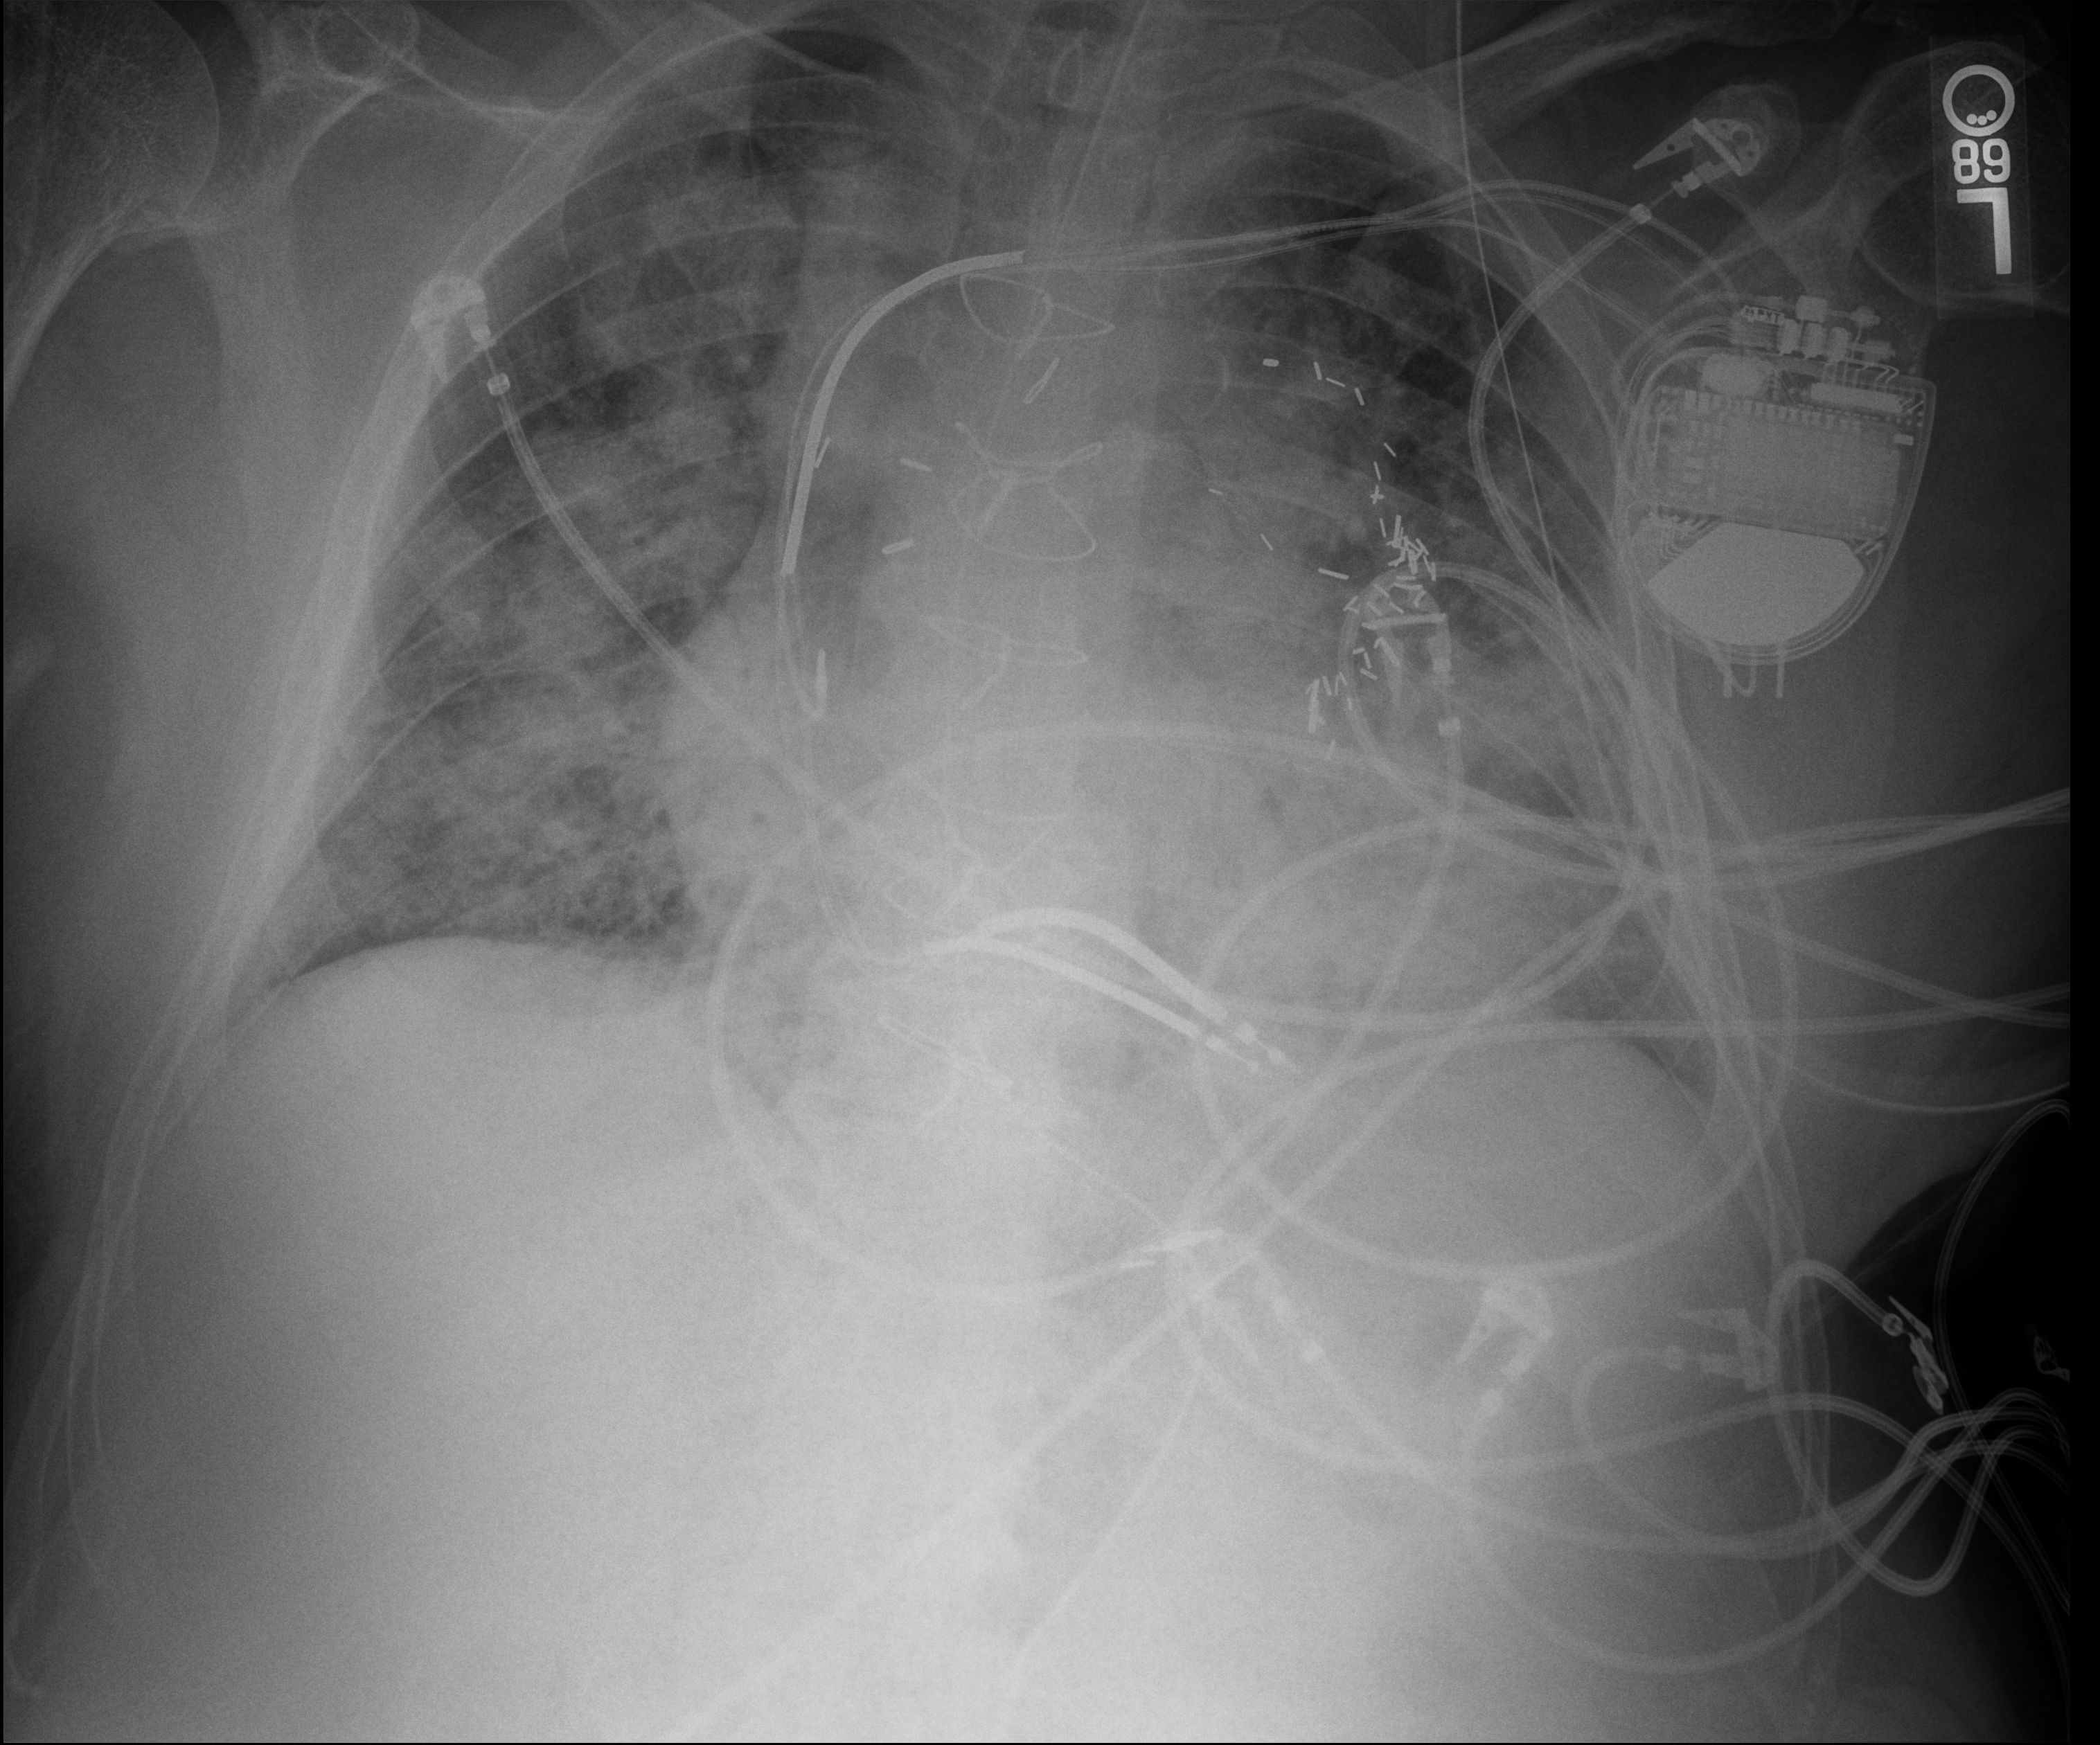
Bedside chest radiograph (digital radiography); anteroposterior (AP) projection. Patient hospitalised with COVID-19; male, aged 60–74 years.
From the hospital-stay record, not from the radiograph (when in the stay this image was taken is not recorded): mechanically ventilated during this hospital stay: yes.